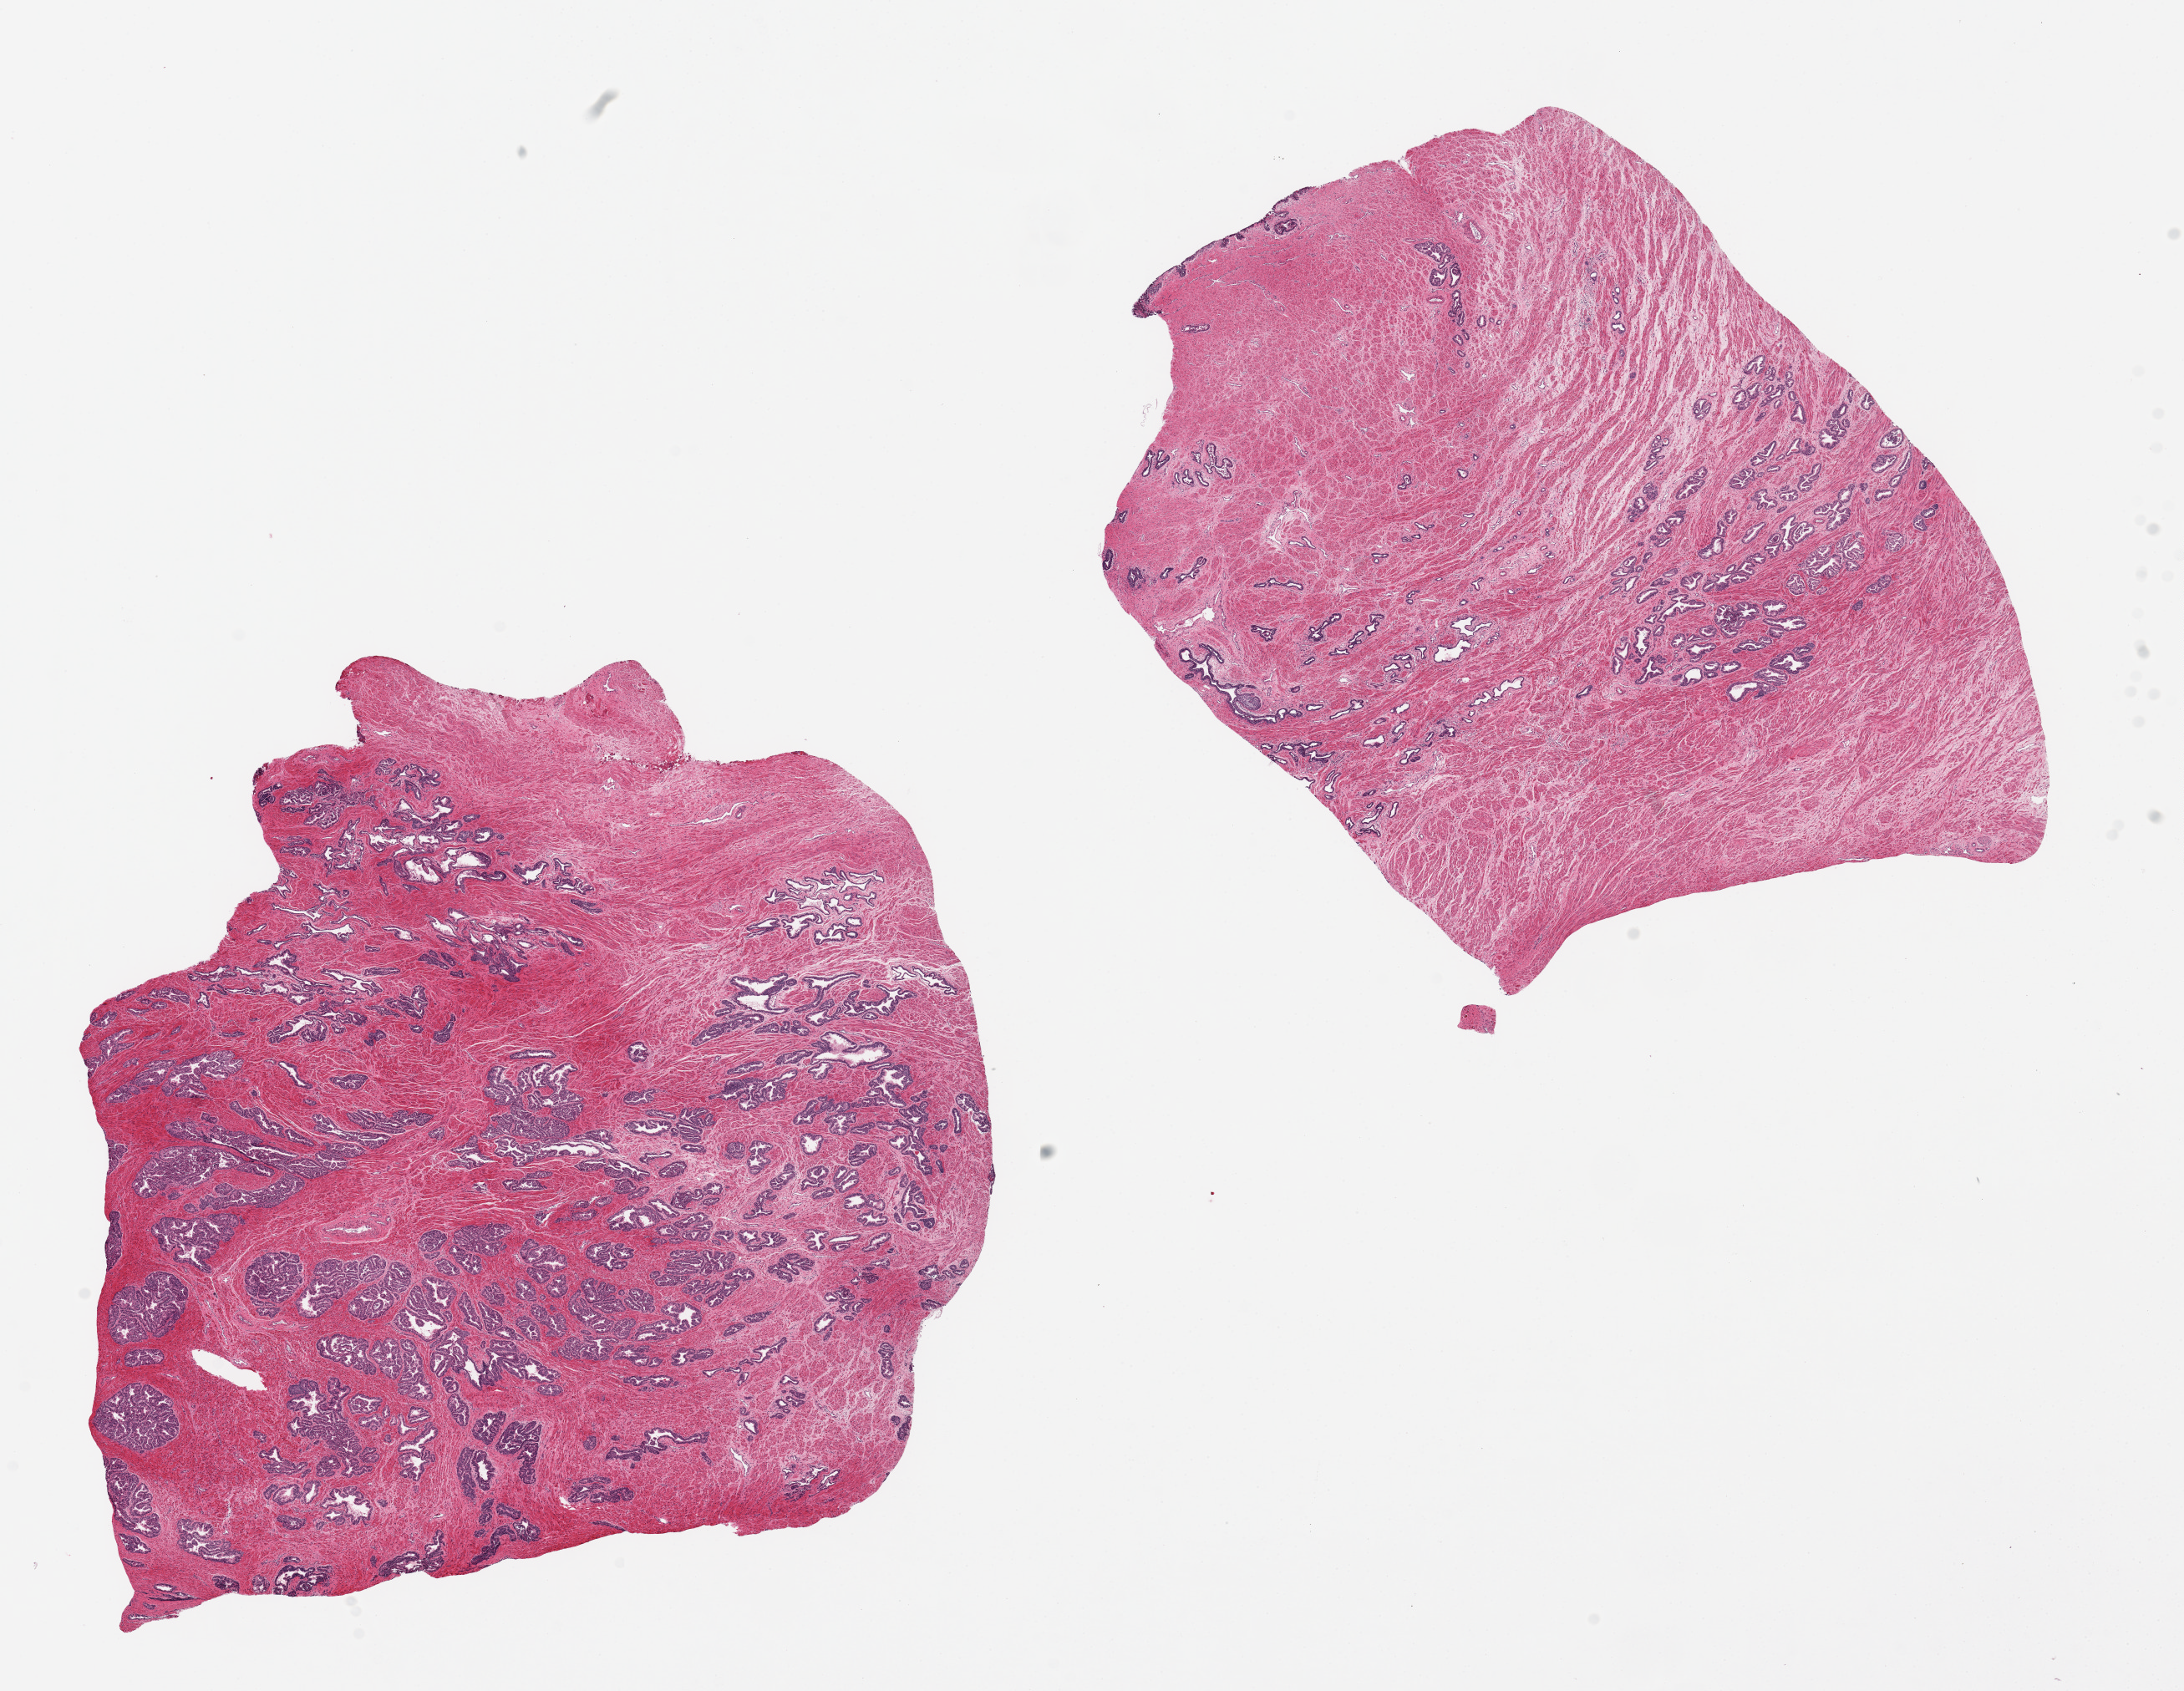
Digitized haematoxylin and eosin-stained section — shown as a low-resolution overview of the whole scanned area (about 20.7 x 16.0 mm, acquisition: 20x scan); PAXgene-fixed paraffin-embedded (PFPE) section; target tissue: prostate; tissue donor sample. Donor: male.
Pathologist's review note for this sample: 2 pieces; 1 piece more glandular than the other; no nodular hyperplasia.